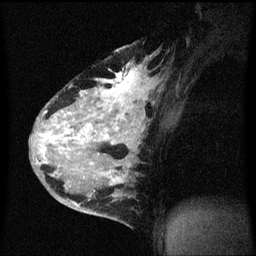
Breast MRI (dynamic contrast-enhanced), one sagittal slice. Position 41 of 60 along the scan axis. Dynamic contrast-enhanced series, image 2 of 3 at this slice position (ordered by acquisition). 1.5 T. TE 4.2 ms, TR 8.4 ms. 2 mm slice thickness. 256 × 256 image matrix. Female patient, age 34 years. Case-level facts recorded for this patient, not image findings: setting: breast cancer imaged before/during neoadjuvant chemotherapy; receptor status: HR-positive, HER2-negative.
Structures marked on this image (semi-automatically segmented with operator editing):
- analysis volume of interest (the breast-tissue region the enhancement analysis was run in; not a lesion): bounding box [x1, y1, x2, y2] px = [34, 48, 157, 215]
- tumour enhancement mask (voxels above the 70 % enhancement threshold inside the analysis volume of interest): [44, 68, 155, 207]